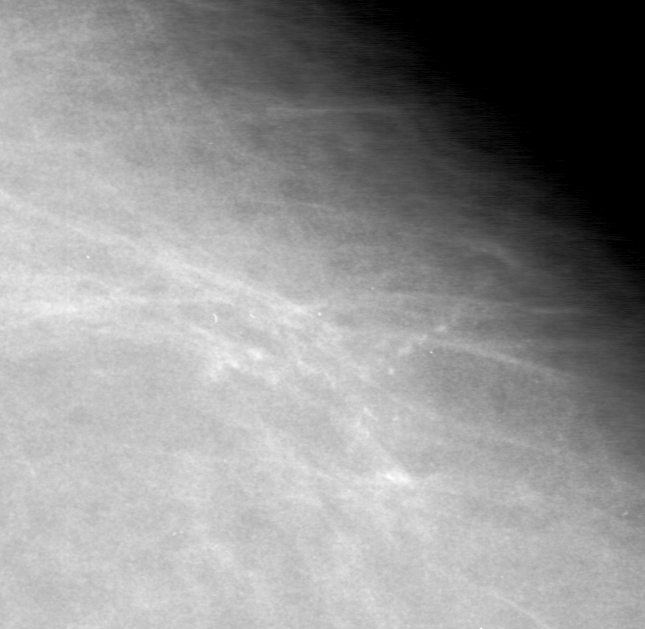
Crop from a digitized film mammogram around one marked abnormality; left breast; CC view.
Calcifications, morphology fine linear branching, distribution clustered; BI-RADS assessment category 0; pathology (as recorded): malignant.